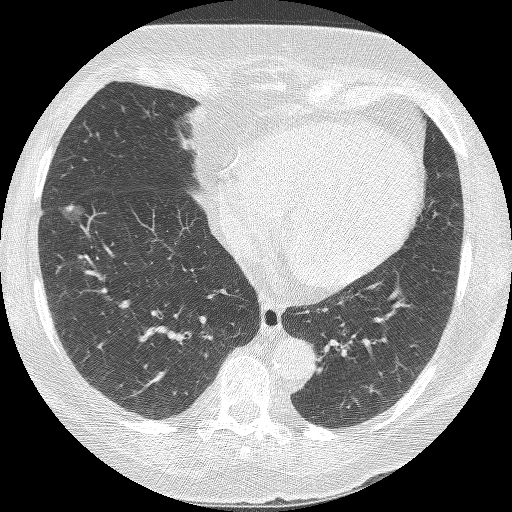
Axial slice from a low-dose chest CT screening exam. Second annual screen. Lung window (W 1500 / L -600 HU). 1.25 mm slice thickness. Lung (sharp) reconstruction kernel (BONE). 120 kVp. Female, age 68 years at enrolment. Current smoker at enrolment.
Expert-annotated lung lesion, bounding box (x1, y1, x2, y2) in pixels: (34, 194, 91, 250). The exam's reader record, not a measurement of the box and not confirmed to be the same lesion: non-calcified nodule or mass ≥4 mm, right lower lobe, 18 × 15 mm, poorly defined margins, ground glass attenuation, pre-existing on the prior screen: yes; interval growth: yes. Official screen result: positive, other. Participant outcome: lung cancer diagnosed 42 days after this screen — bronchiolo-alveolar adenocarcinoma, NOS, right lower lobe, well differentiated (G1), stage IA (AJCC 6th edition), 13 mm at pathology.